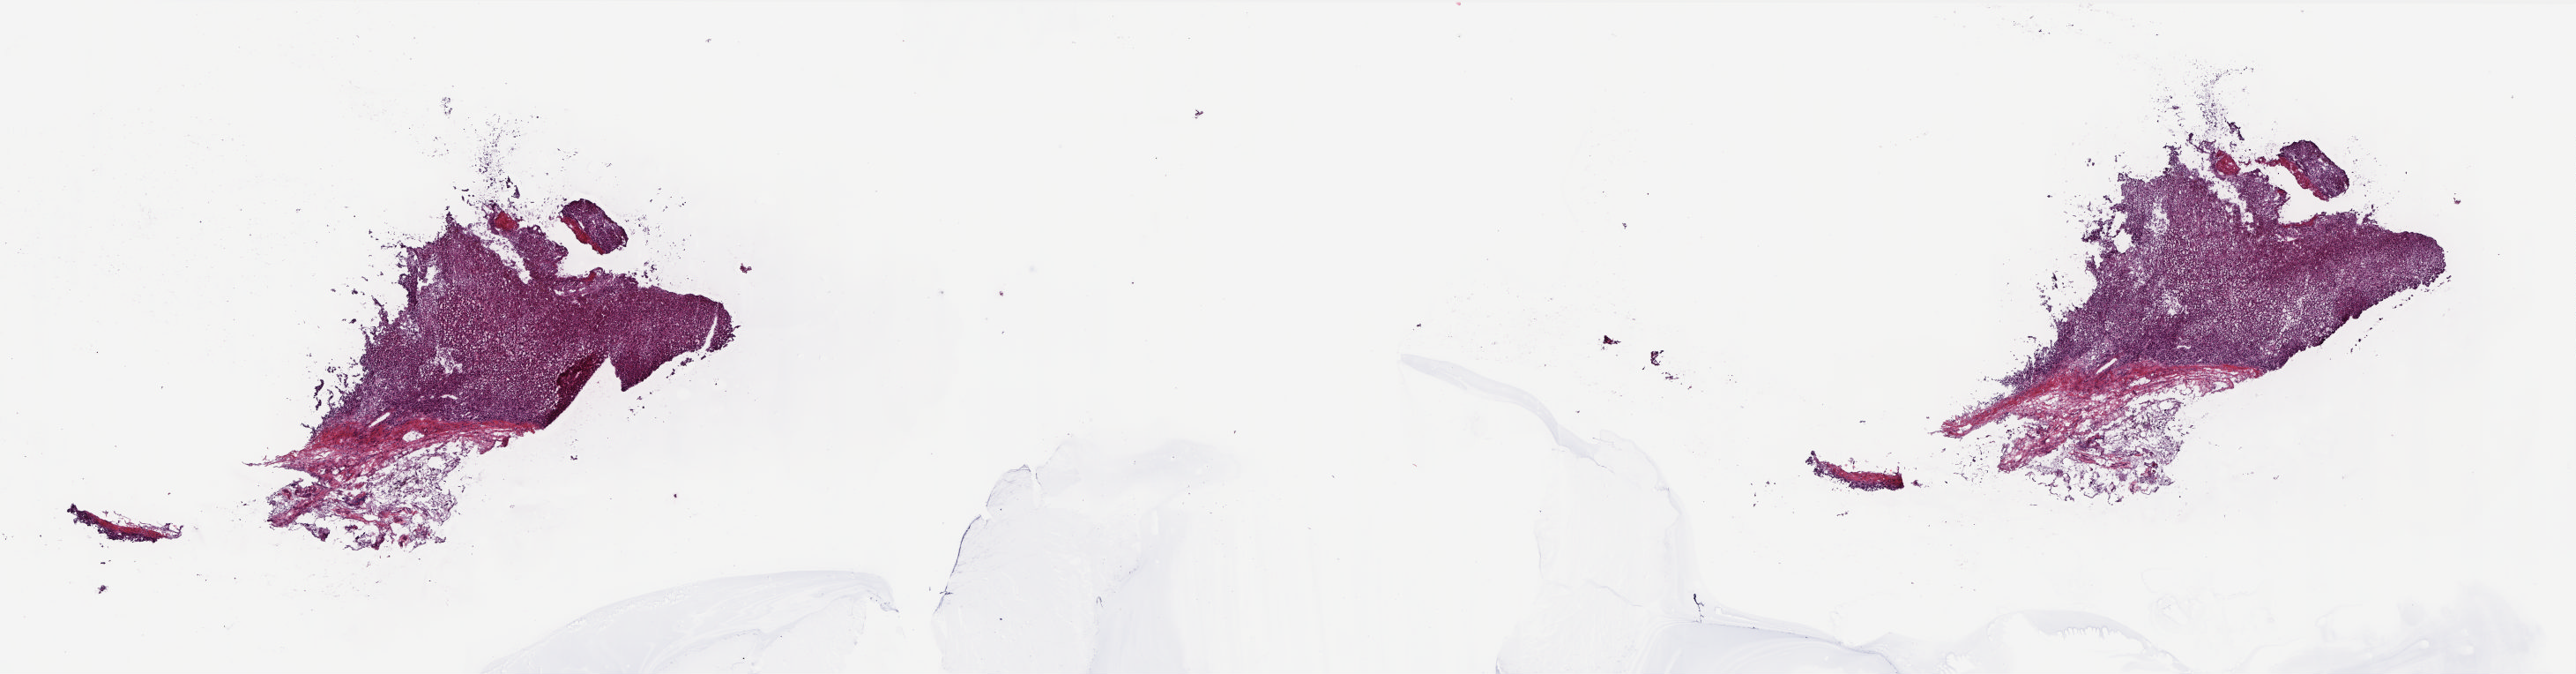
Digitized H&E-stained tissue section (whole slide) — low-resolution overview of the scanned area, about 23.6 x 6.2 mm (acquisition: 20x scan), frozen section, solid tissue normal (non-tumour tissue) sample from the adrenal gland. Patient: male, age at initial diagnosis 48 years. Pathologist review of this section (percent, as recorded): tumour cells 0%, tumour nuclei 0%, normal cells 100%, stromal cells 0%, necrosis 0%. Infiltration values recorded for this section: lymphocyte infiltration 1%, monocyte infiltration 0%, neutrophil infiltration 0%.
* this section: solid tissue normal (non-tumour) sample from the same patient
* patient diagnosis: Pheochromocytoma, NOS